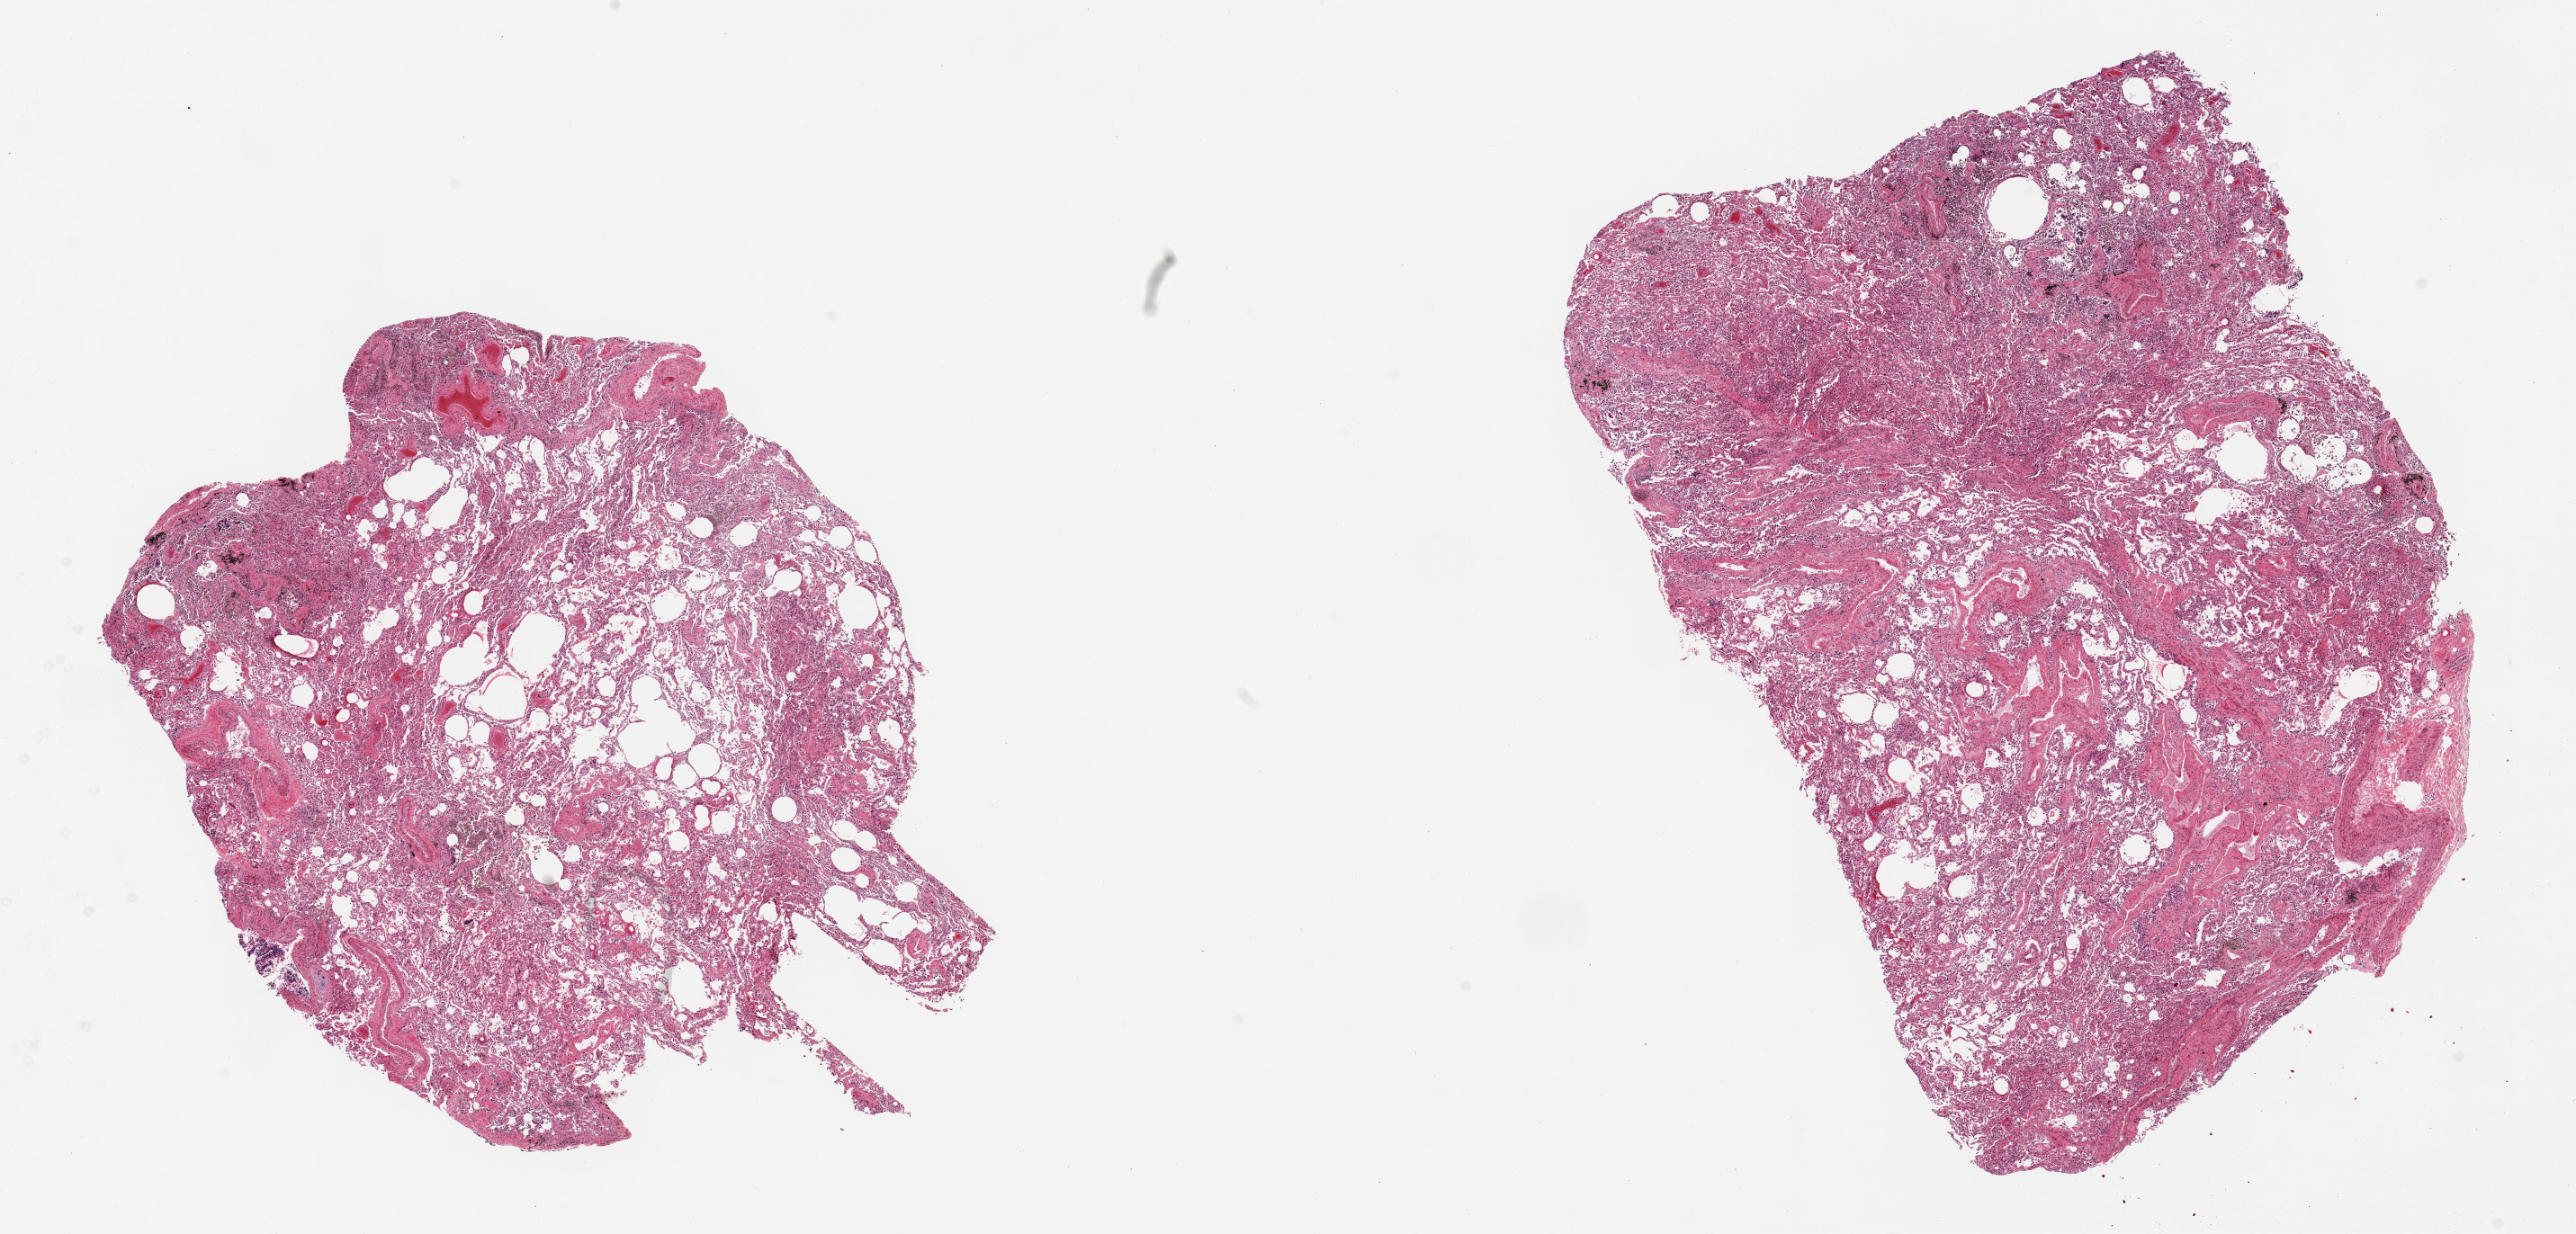
Whole-slide image, haematoxylin and eosin stain — a low-resolution overview of the entire scanned area, about 22.6 x 10.9 mm (slide scanned at 20x). PAXgene-fixed paraffin-embedded (PFPE) section. Target tissue: lung. Tissue donor sample. Male donor.
Reviewer comment on this tissue sample: 2 pieces, moderate congestion, evidence of chronic congestive heart failure (hemosiderin laden macrophages).